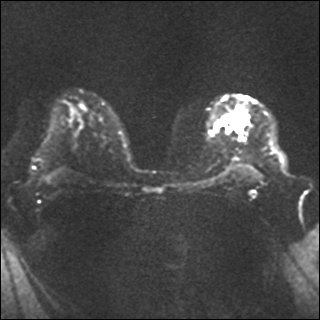
Breast MRI, one axial slice. Position 23 of 35 along the scan axis. Diffusion-weighted series; image 2 of 4 stored at this slice position (different b-values; order by instance number). 1.5 T. 4 mm slice thickness. 320 × 320 image matrix, field of view 320 × 320 mm. Female patient.
Annotated regions visible in this slice (outlined manually by an expert reader):
- tumour on diffusion-weighted imaging: bounding box <229,117,241,131> (left, top, right, bottom; pixels)